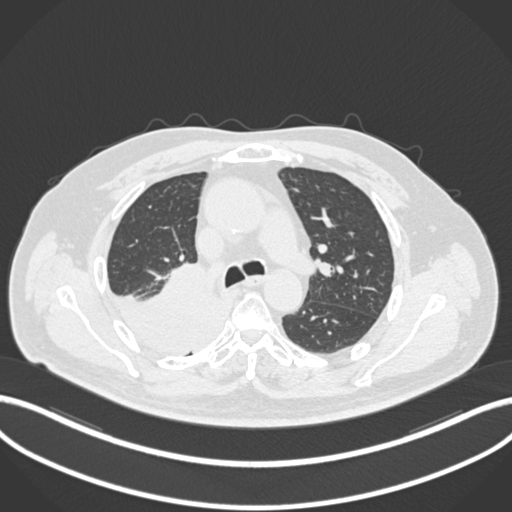
Chest CT, one axial slice; position 133 of 218 along the scan axis; 120 kVp; lung window (W 1500 / L -600 HU); 512 × 512 image matrix, field of view 400 × 400 mm. Male patient, age 68 years. Case-level facts recorded for this patient, not image findings: clinical TNM (as recorded): T2a N0 M0.
Outlined on this slice (rectangle marked by the reading radiologist):
- lung tumour (recorded histology: adenocarcinoma): bounding box (x1, y1, x2, y2) in pixels: (111, 264, 230, 356)